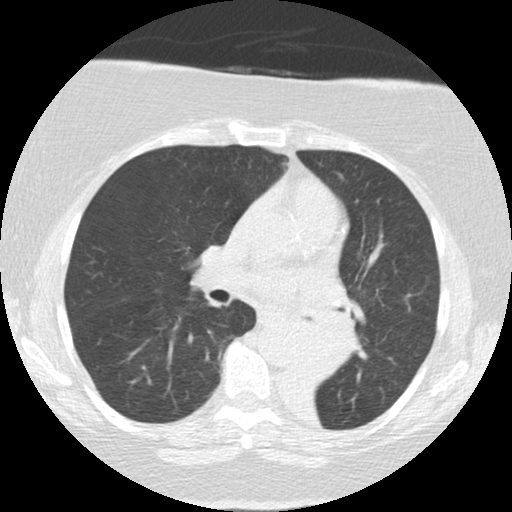
Chest CT (low-dose screening protocol), one axial image; baseline annual screen; lung window (W 1500 / L -600 HU); 2.5 mm slice thickness; standard (soft-tissue) reconstruction kernel (STANDARD); 120 kVp; slice 61 of 136 in the series; 512 × 512 image matrix, field of view 309 × 309 mm. Female participant, aged 71 years at enrolment. Former smoker at enrolment.
• Lesion marked by an expert reader, box from (x=287, y=308) to (x=363, y=383) px.
• Screening reader's record for this exam (one nodule recorded; not confirmed to be the boxed lesion): non-calcified nodule or mass ≥4 mm, right middle lobe, 5 × 5 mm, smooth margins, soft tissue attenuation.
• Note: the box lies in the patient's left hemithorax on this image, whereas the reader's record names the right lung; they may be different findings.
• Later outcome: lung cancer diagnosed 46 days after this screen — large cell carcinoma, NOS, left lower lobe, mediastinum, other location, poorly differentiated (G3), stage IV (AJCC 6th edition), 50 mm at pathology.